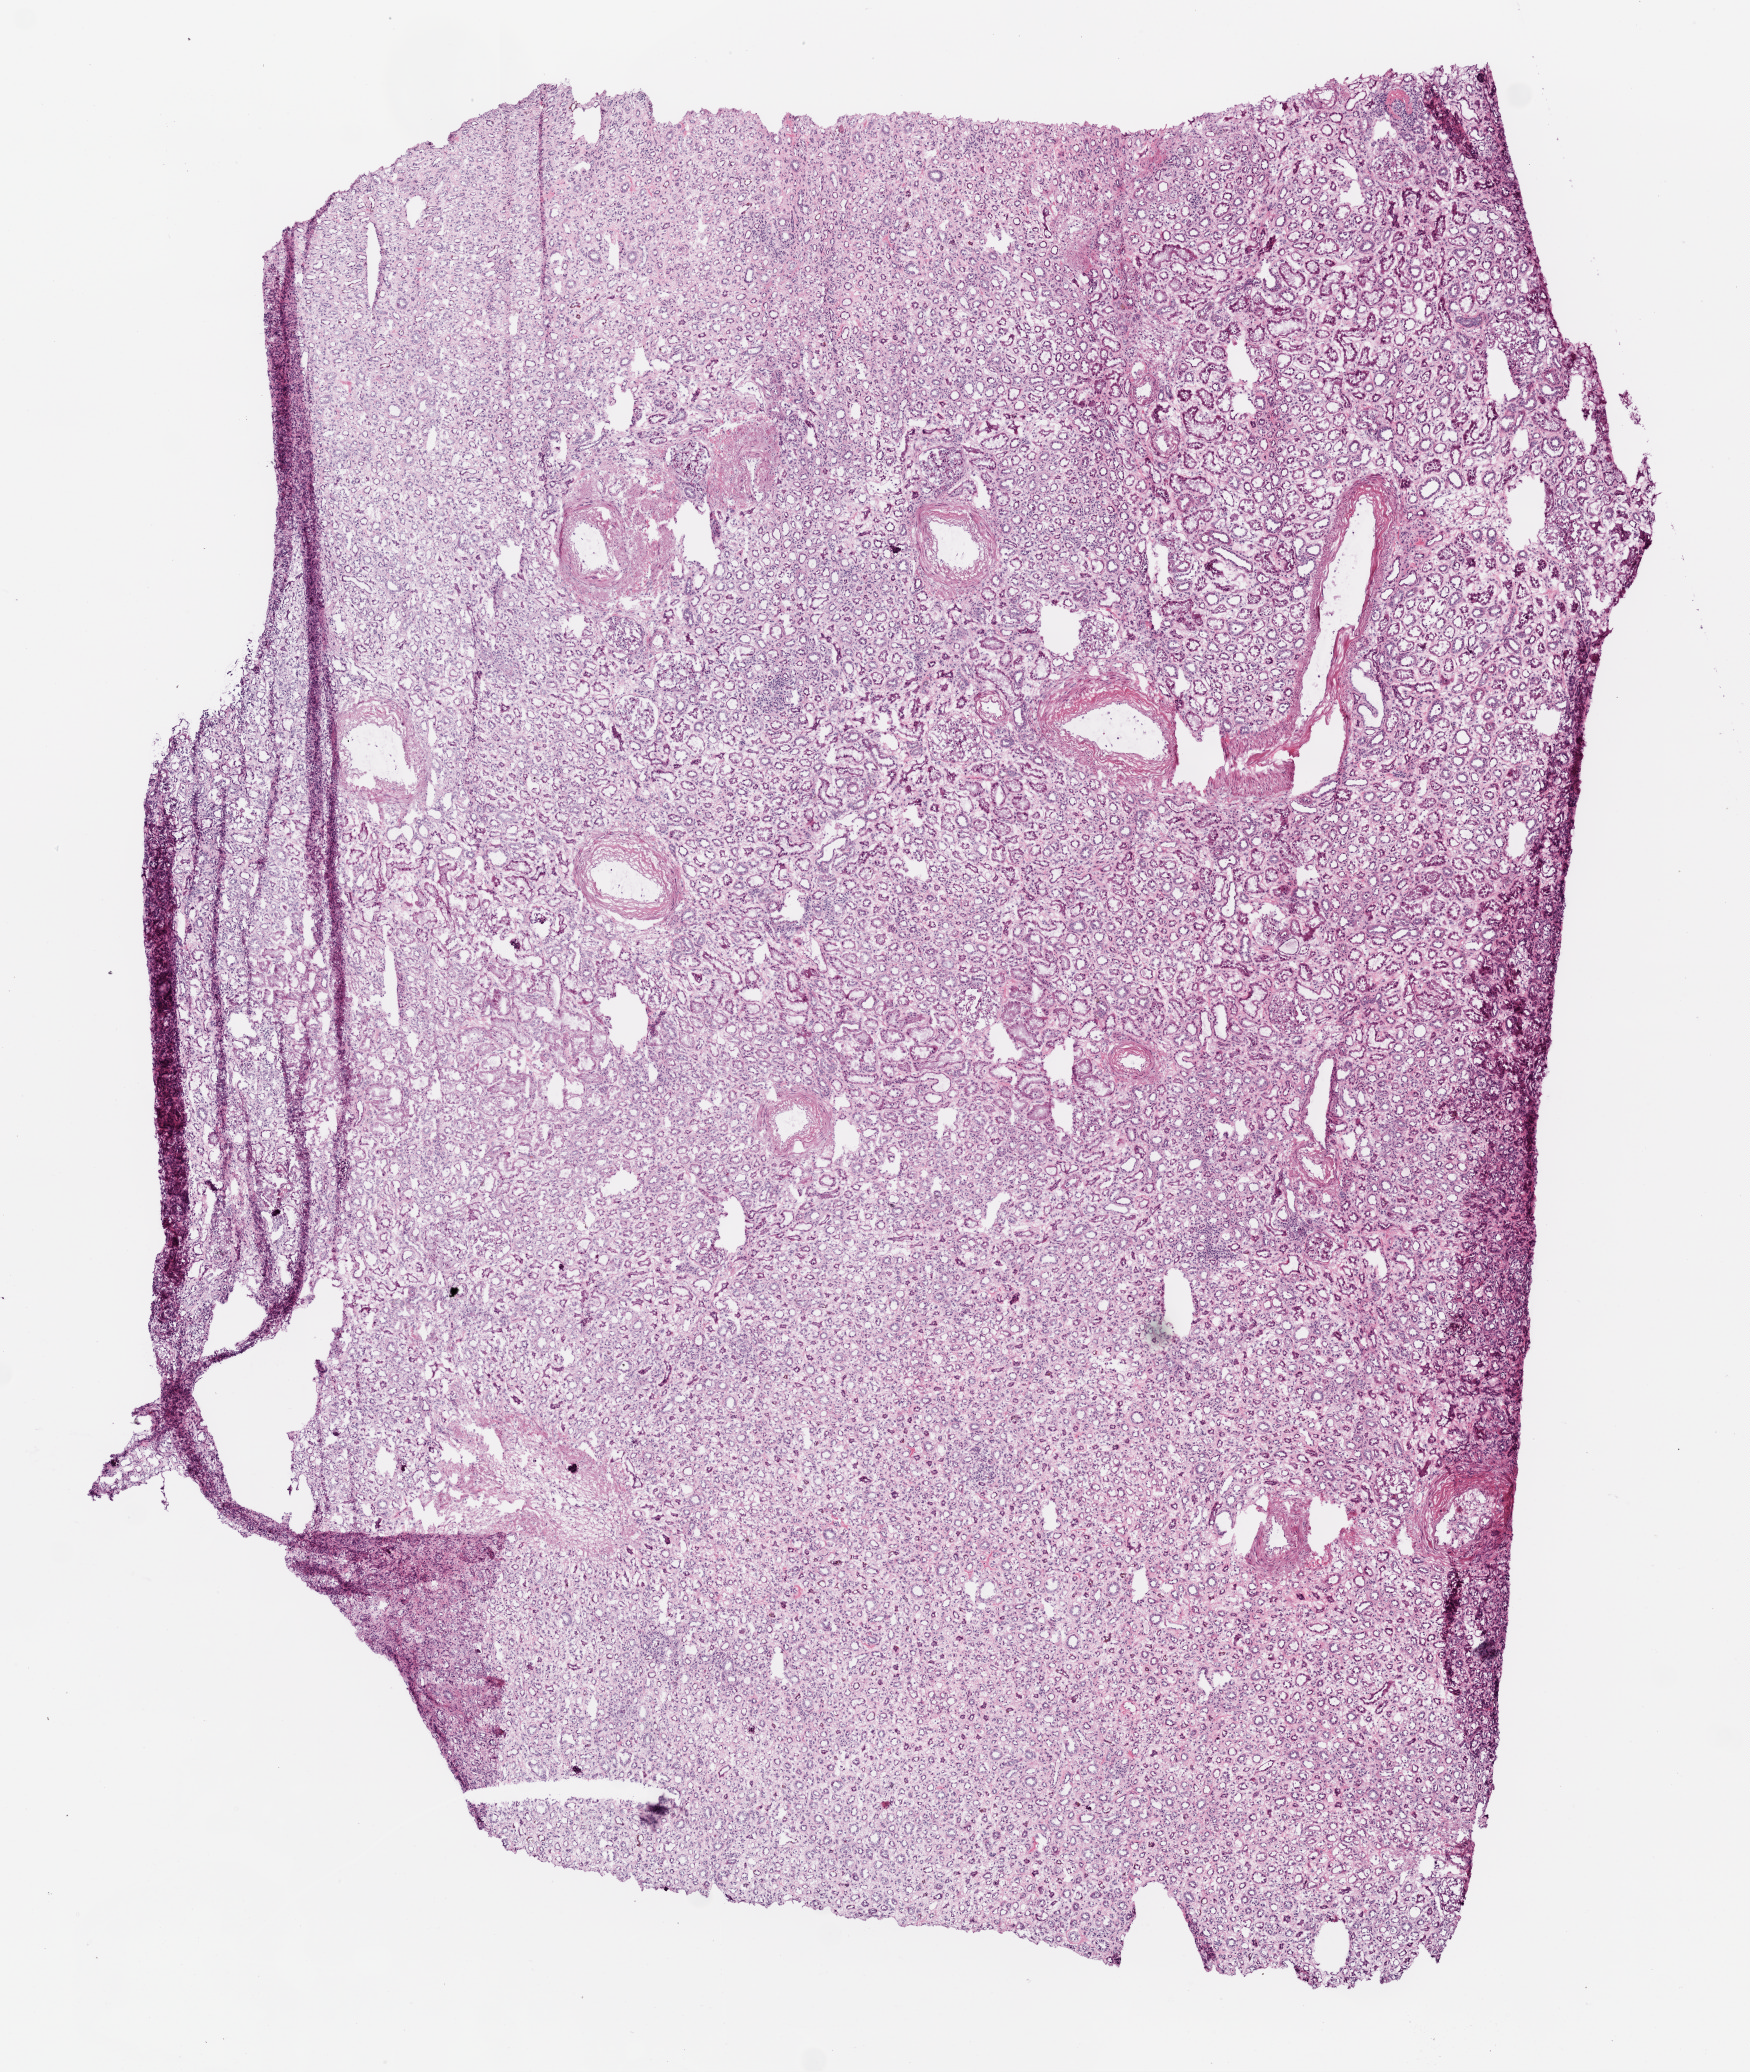
Digitized Hematoxylin and eosin (H&E) stained tissue section (whole slide) — a low-resolution overview of the entire scanned area, about 7.0 x 8.3 mm, frozen section from the top of the tissue portion, solid tissue normal (non-tumour tissue) sample from the kidney. Female patient; age at initial diagnosis 66 years.
This section: solid tissue normal (non-tumour) sample from the same patient. Patient diagnosis: Clear cell adenocarcinoma, NOS.